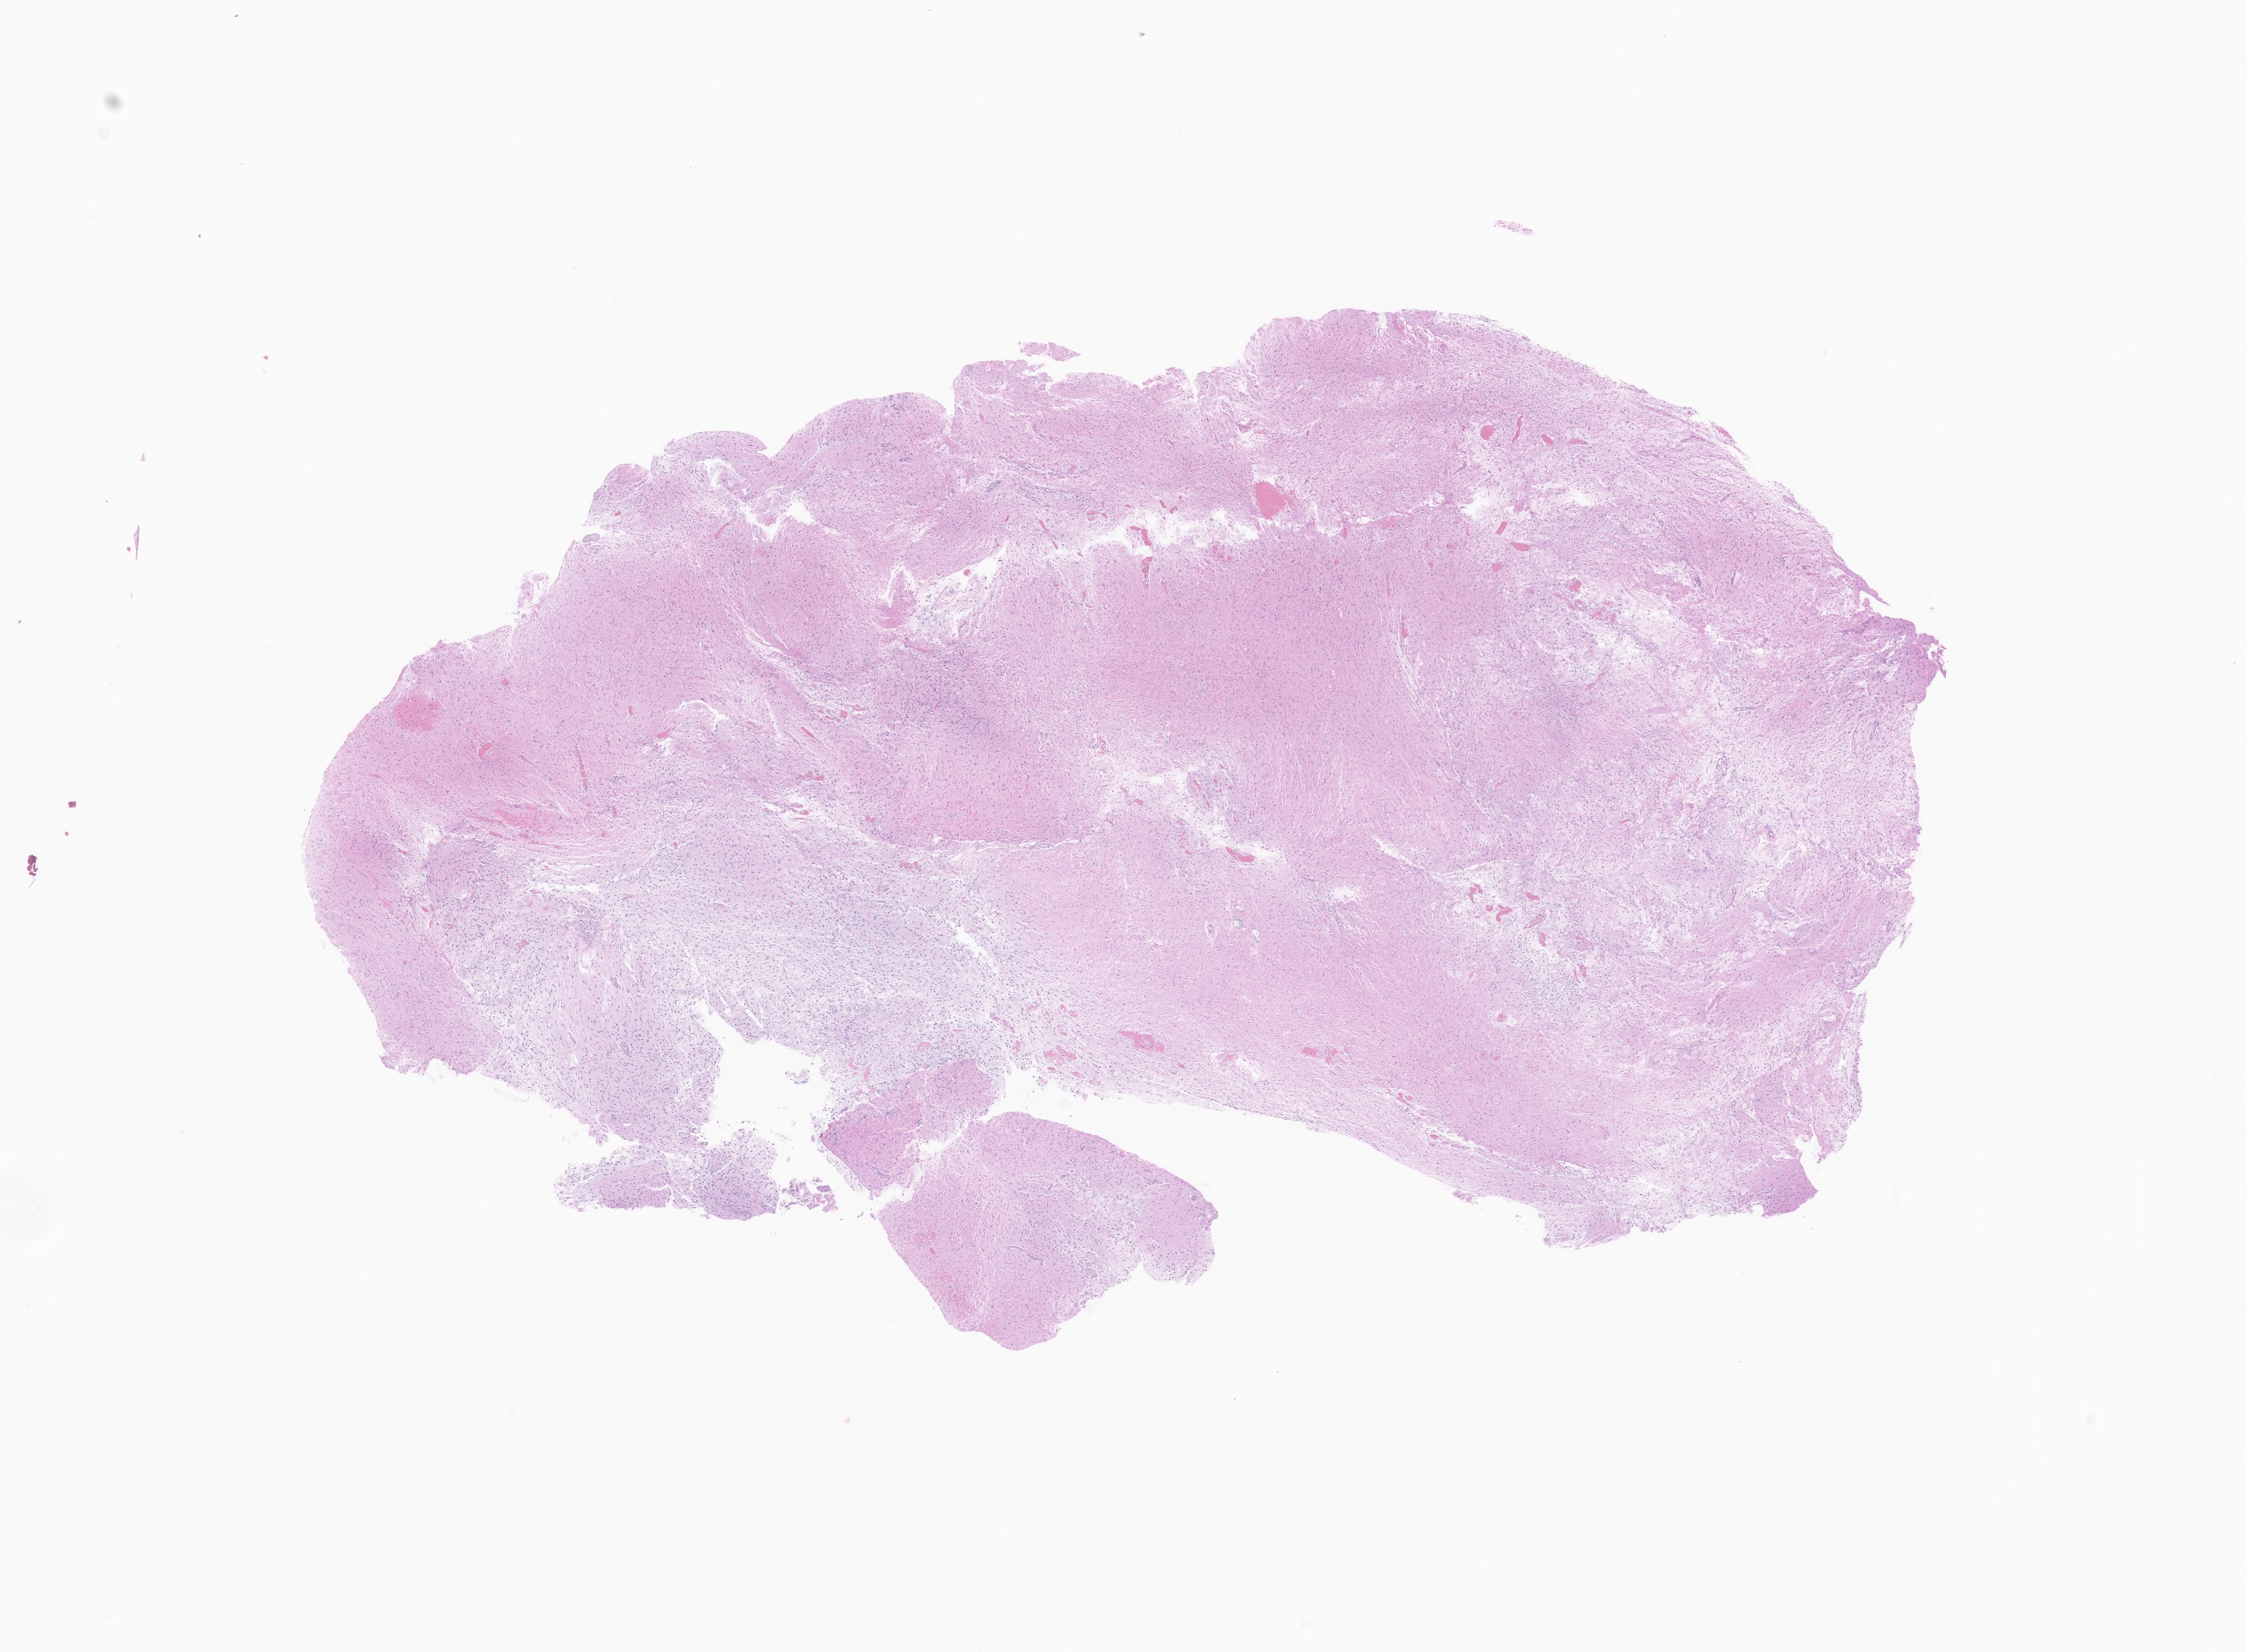
Digitized haematoxylin and eosin-stained section of tumor tissue from the brain — whole scanned area (about 13.7 x 10.1 mm) shown as a low-resolution overview. Formalin-fixed, paraffin-embedded (FFPE) tissue. Female patient, age 69 months (5 years 9 months).
Recorded diagnosis: Glioma, malignant.